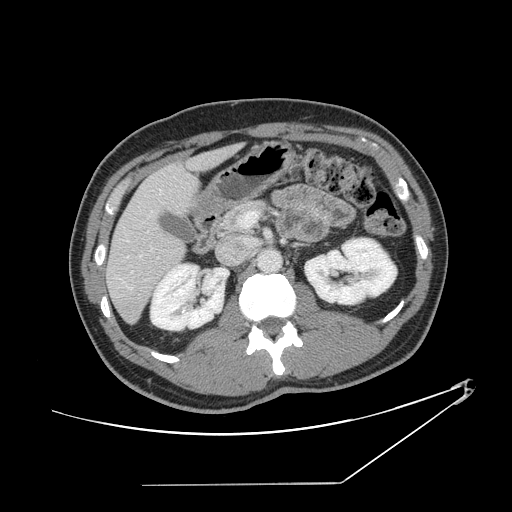
Contrast-enhanced abdominal CT, one axial slice. Slice 69 of 152 in the series (ordered by position). Reconstruction kernel STANDARD. 120 kVp. Intravenous contrast given. Soft-tissue window (W 400 / L 40 HU). 2.5 mm slice thickness. 512 × 512 image matrix, field of view 432 × 432 mm. Male patient, age 45 years. Case-level facts recorded for this patient, not image findings: diagnosis: colorectal cancer liver metastases, imaged before liver resection; multiple liver metastases: no; largest metastasis: 1 cm.
Structures marked on this image (expert manual segmentation):
- hepatic veins: bounding box [x1, y1, x2, y2] px = [124, 189, 162, 289]
- liver: [107, 146, 237, 322]
- planned liver remnant (the part of the liver to remain after resection): [107, 164, 198, 322]
- portal vein (with intrahepatic branches): [239, 211, 258, 228]